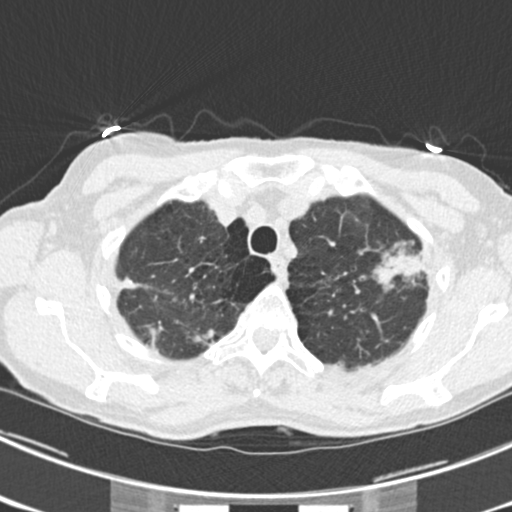
Low-dose screening chest CT, axial slice. Third screening round (two years after baseline). Lung window (W 1500 / L -600 HU). Slice 42 of 225 in the series. Female participant, aged 63 years at enrolment. Current smoker at enrolment.
Expert-annotated lung lesion, bounding box (x1, y1, x2, y2) in pixels: (374, 237, 441, 299). The screening reader recorded 9 non-calcified nodules or masses ≥4 mm on this exam (left upper lobe, right upper lobe, left upper lobe, left lower lobe, right middle lobe, left lower lobe, left lower lobe, right lower lobe, right lower lobe); which of them this box marks is not recorded. Official screen result: positive, other. Lung cancer was diagnosed 15 days after this screen: bronchiolo-alveolar adenocarcinoma, NOS, right upper lobe, right middle lobe, right lower lobe, left upper lobe, left lower lobe, moderately differentiated (G2), stage IV (AJCC 6th edition).